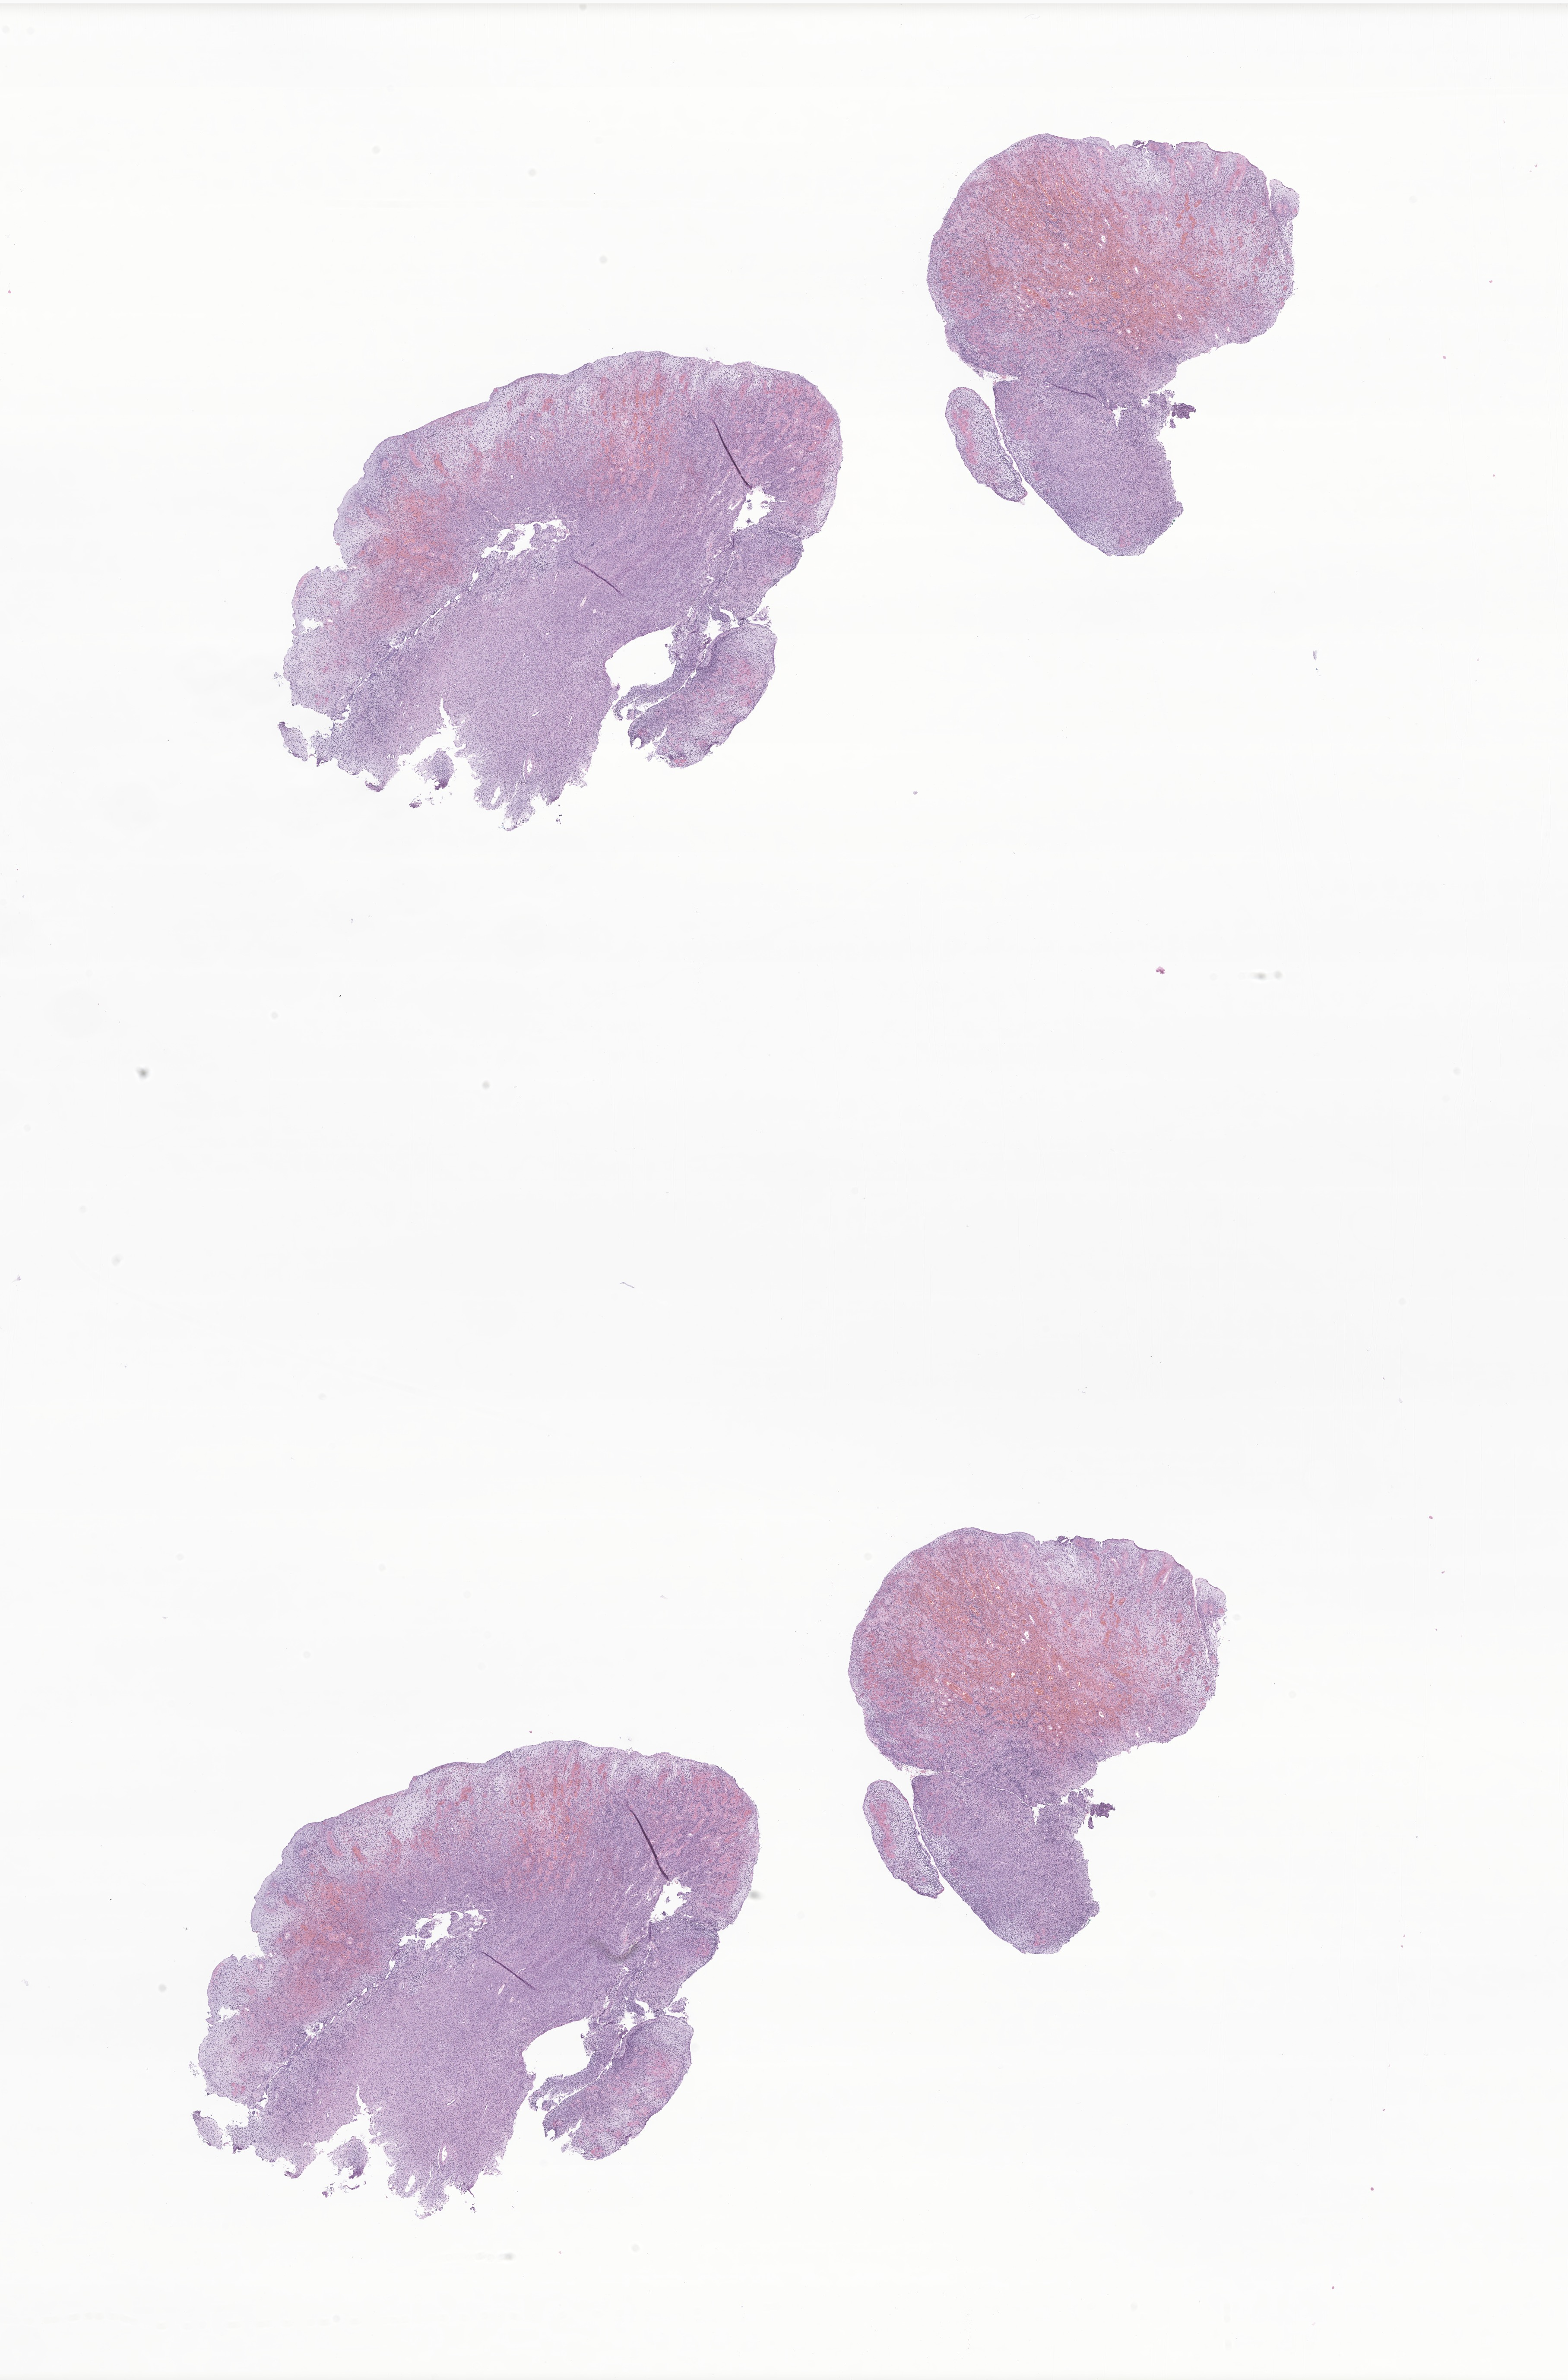
Whole-slide image, H&E stain of tumor tissue from the urinary bladder, low-resolution overview of the scanned area, about 15.3 x 23.2 mm; formalin-fixed, paraffin-embedded (FFPE) tissue. Patient: female, age 652 days.
* recorded diagnosis: Rhabdomyosarcoma, NOS